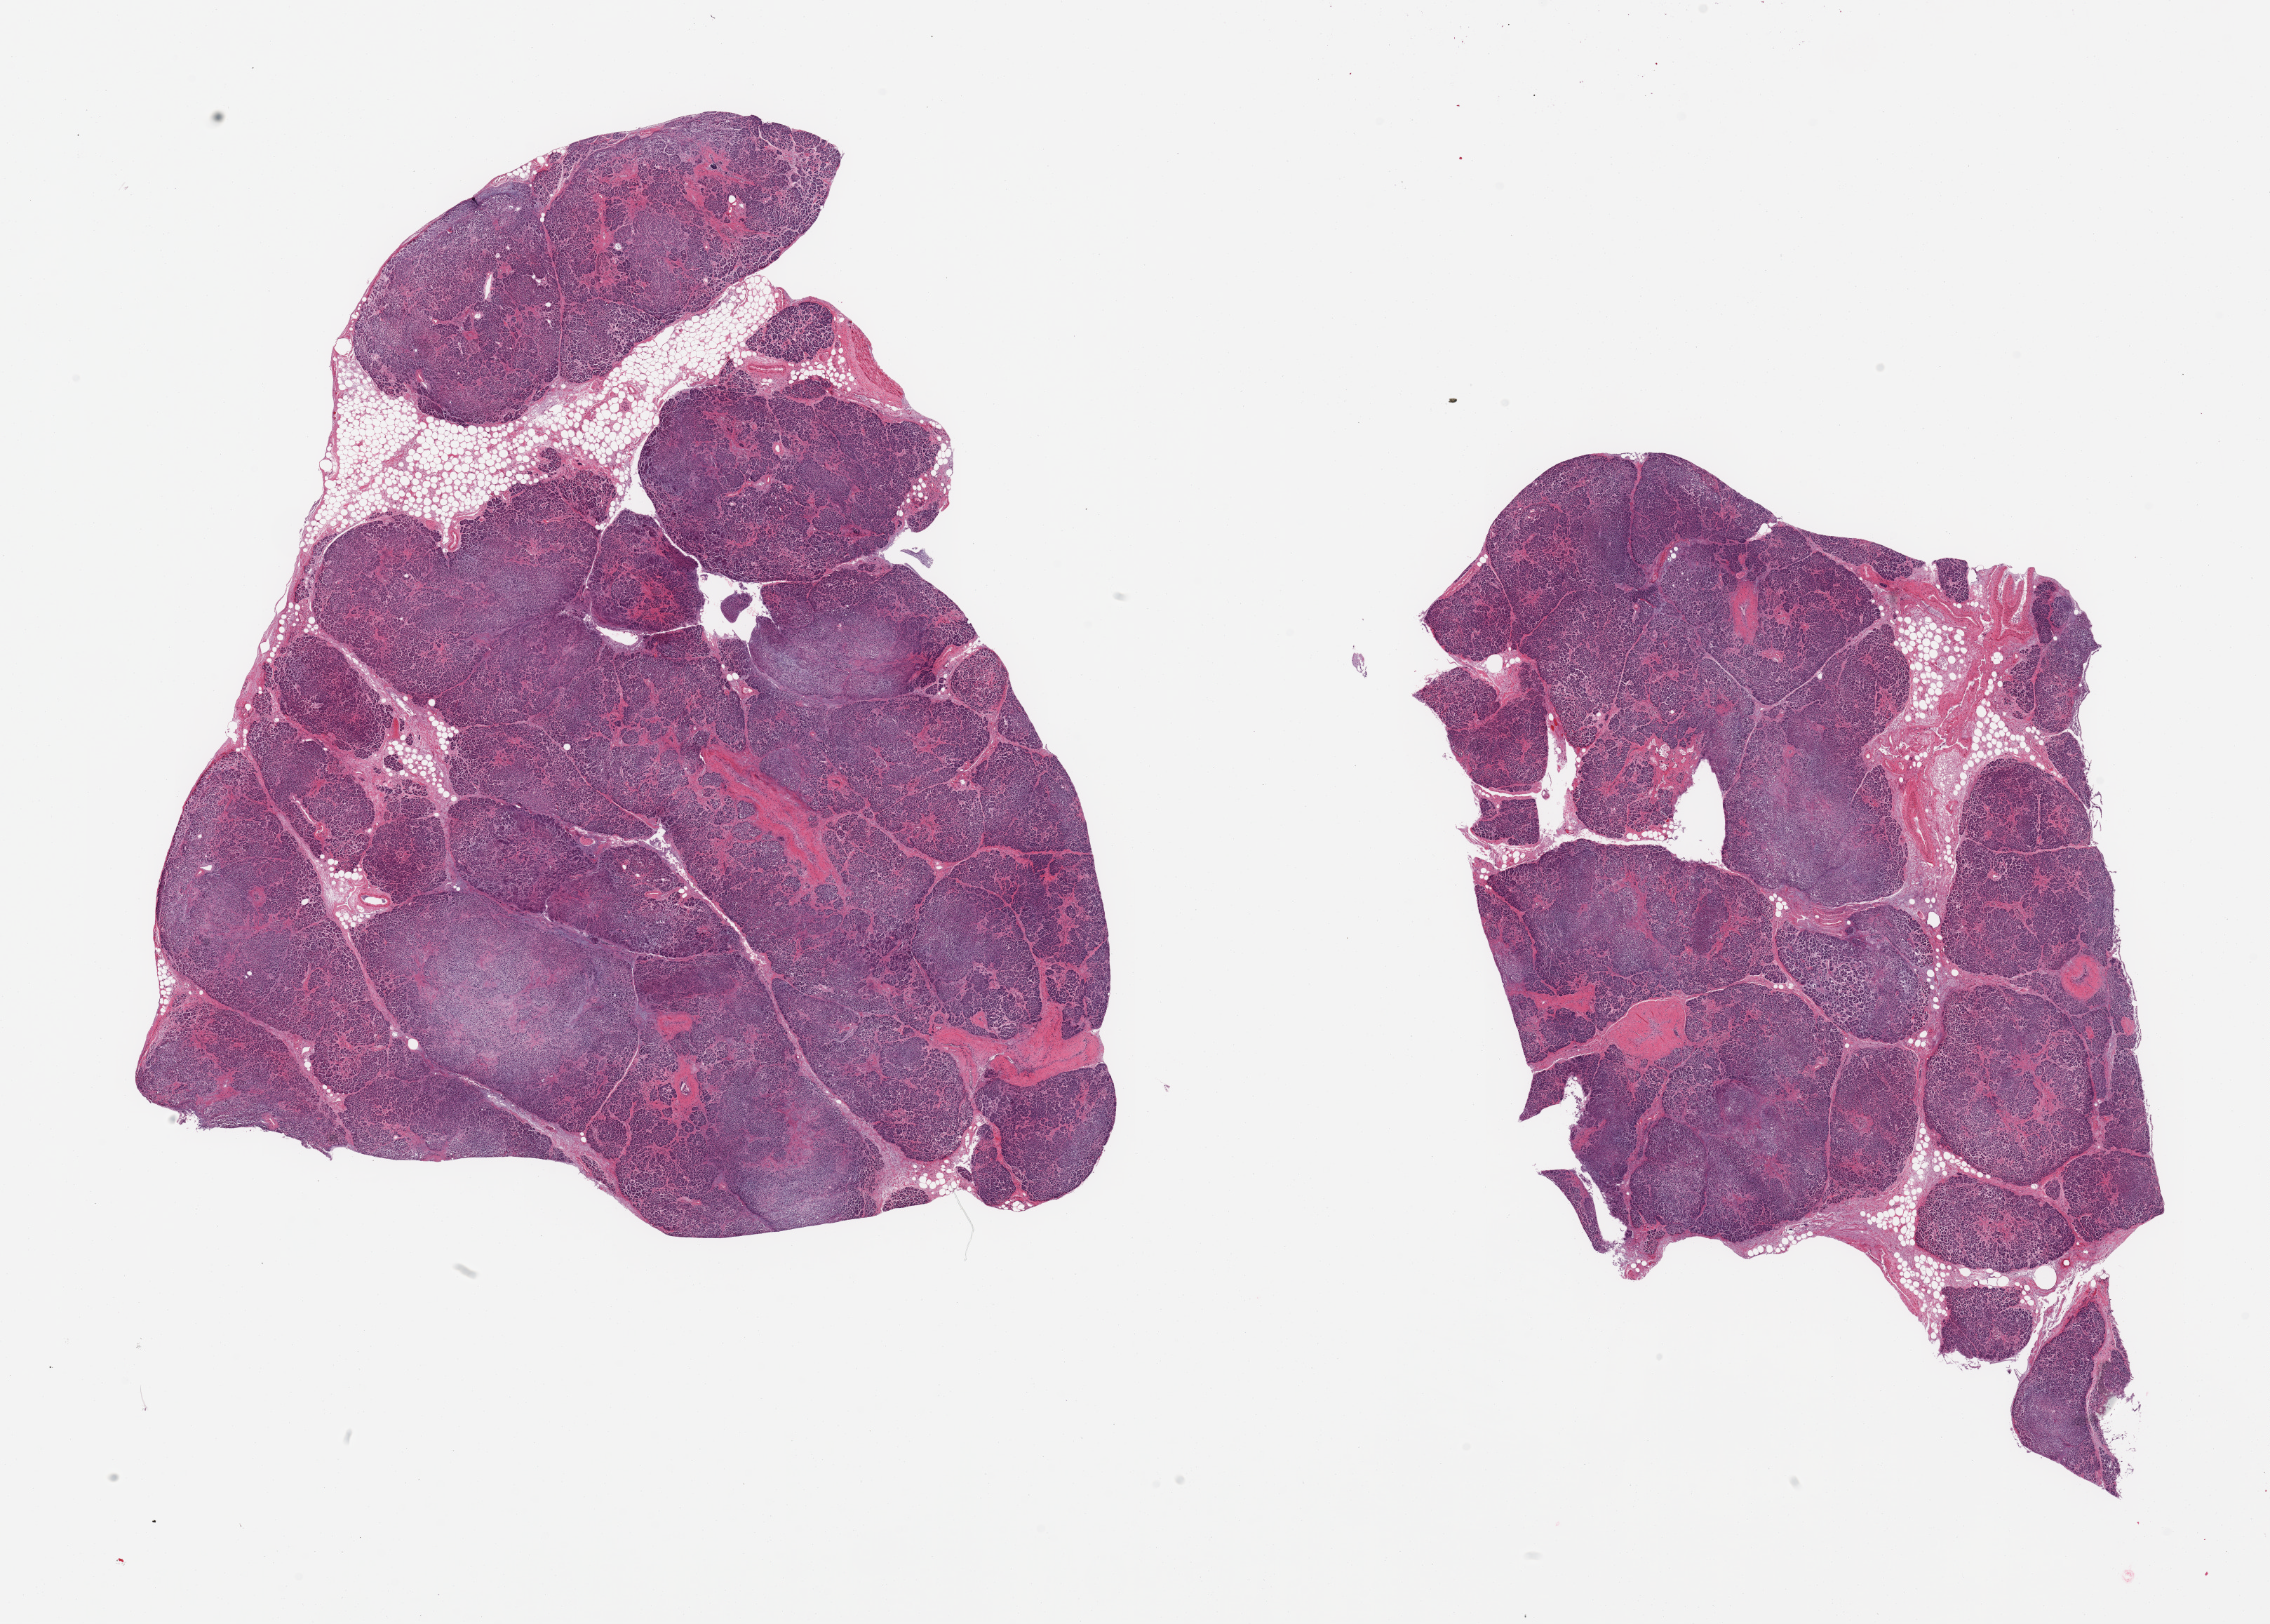
Hematoxylin and eosin (H&E) whole-slide image, a low-resolution overview of the entire scanned area, about 25.6 x 18.3 mm (acquisition: 20x scan); PAXgene-fixed paraffin-embedded (PFPE) section; sampled site (target tissue): pancreas; tissue donor sample. Donor sex: male.
Review note (as recorded): 2 pieces, moderately advanced saponification; Islets not well visualized.